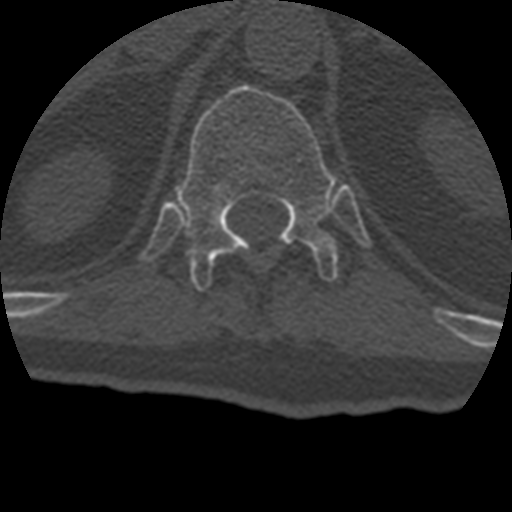
CT including the spine, one axial slice; position 180 of 399 along the scan axis; reconstruction kernel STANDARD; 120 kVp; bone window (W 1800 / L 400 HU); 1.25 mm slice thickness; 512 × 512 image matrix, field of view 160 × 160 mm. Patient age 69 years. Case-level facts recorded for this patient, not image findings: primary cancer: prostate.
Outlined on this slice (semi-automatic segmentation, software-assisted and operator-edited):
- T12 vertebra: bounding box (x1, y1, x2, y2) in pixels: (176, 84, 339, 290)